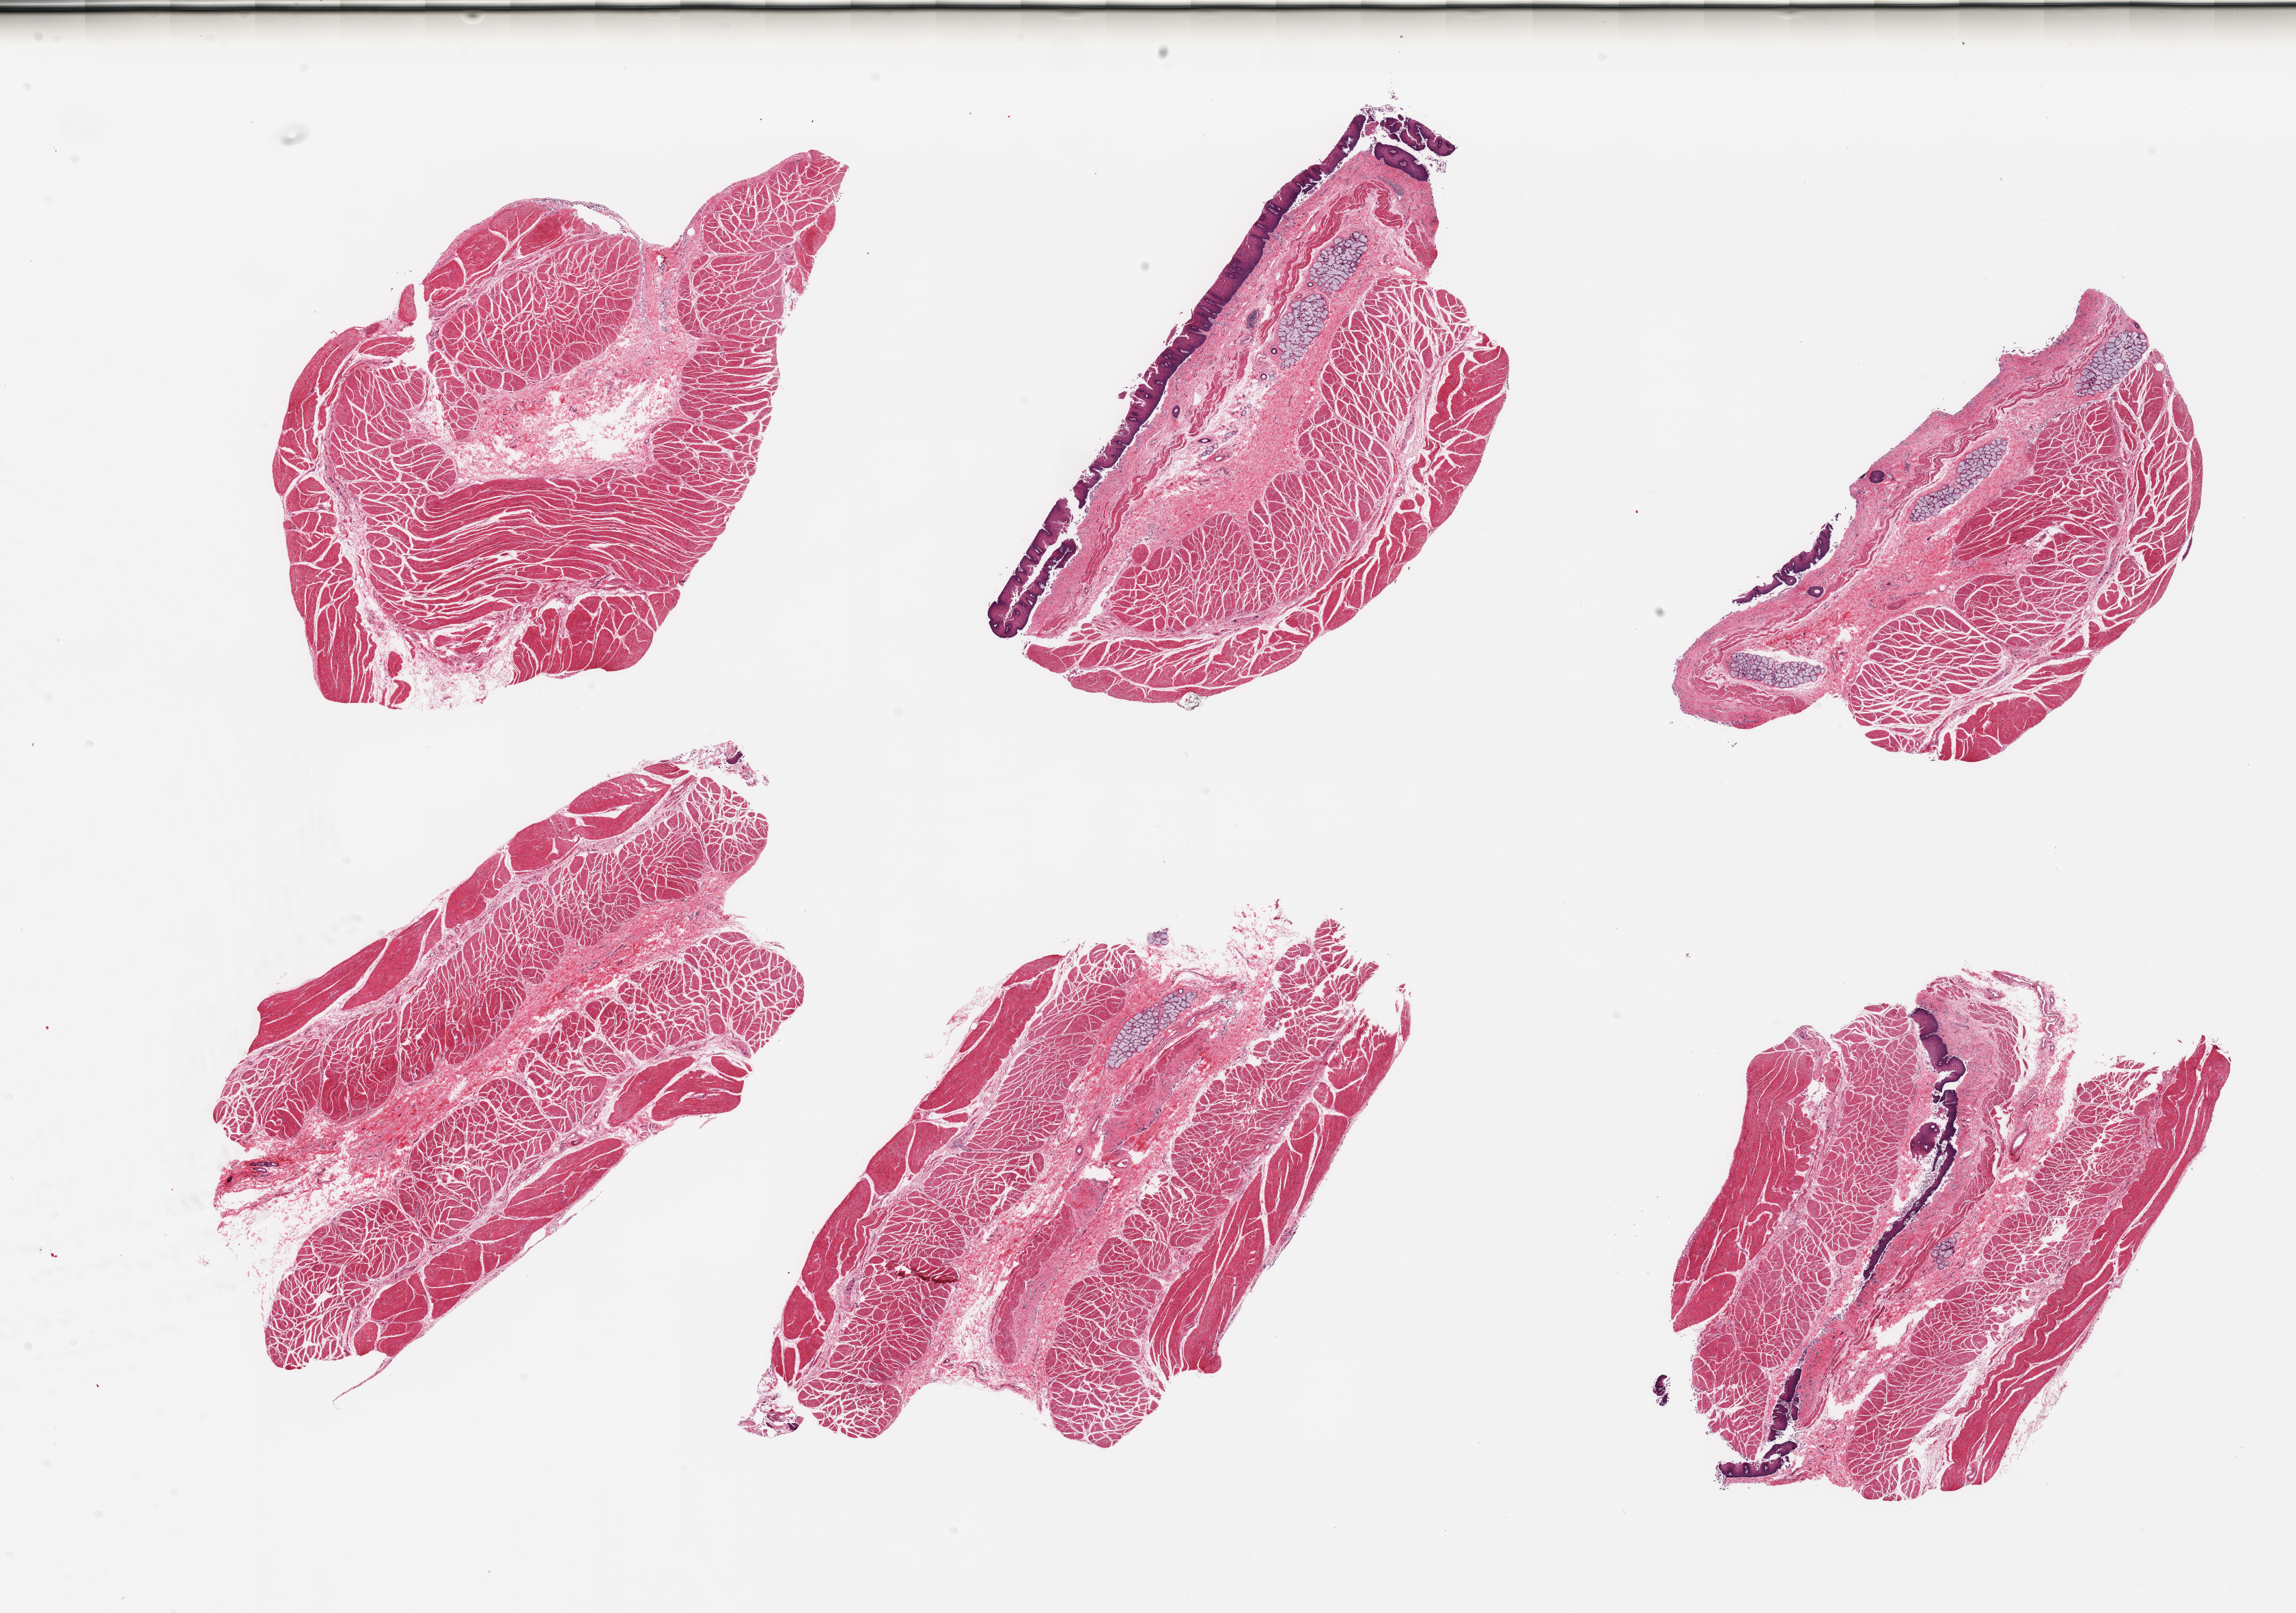
Digitized hematoxylin and eosin (H&E)-stained section — shown as a low-resolution overview of the whole scanned area (about 26.6 x 18.7 mm); PAXgene-fixed paraffin-embedded (PFPE) section; sampled site (target tissue): esophageal muscle; tissue donor sample.
- pathologist's review note for this sample: 6 pieces, few foci of squamous mucosa, confiremd target muscularis; mucos glands